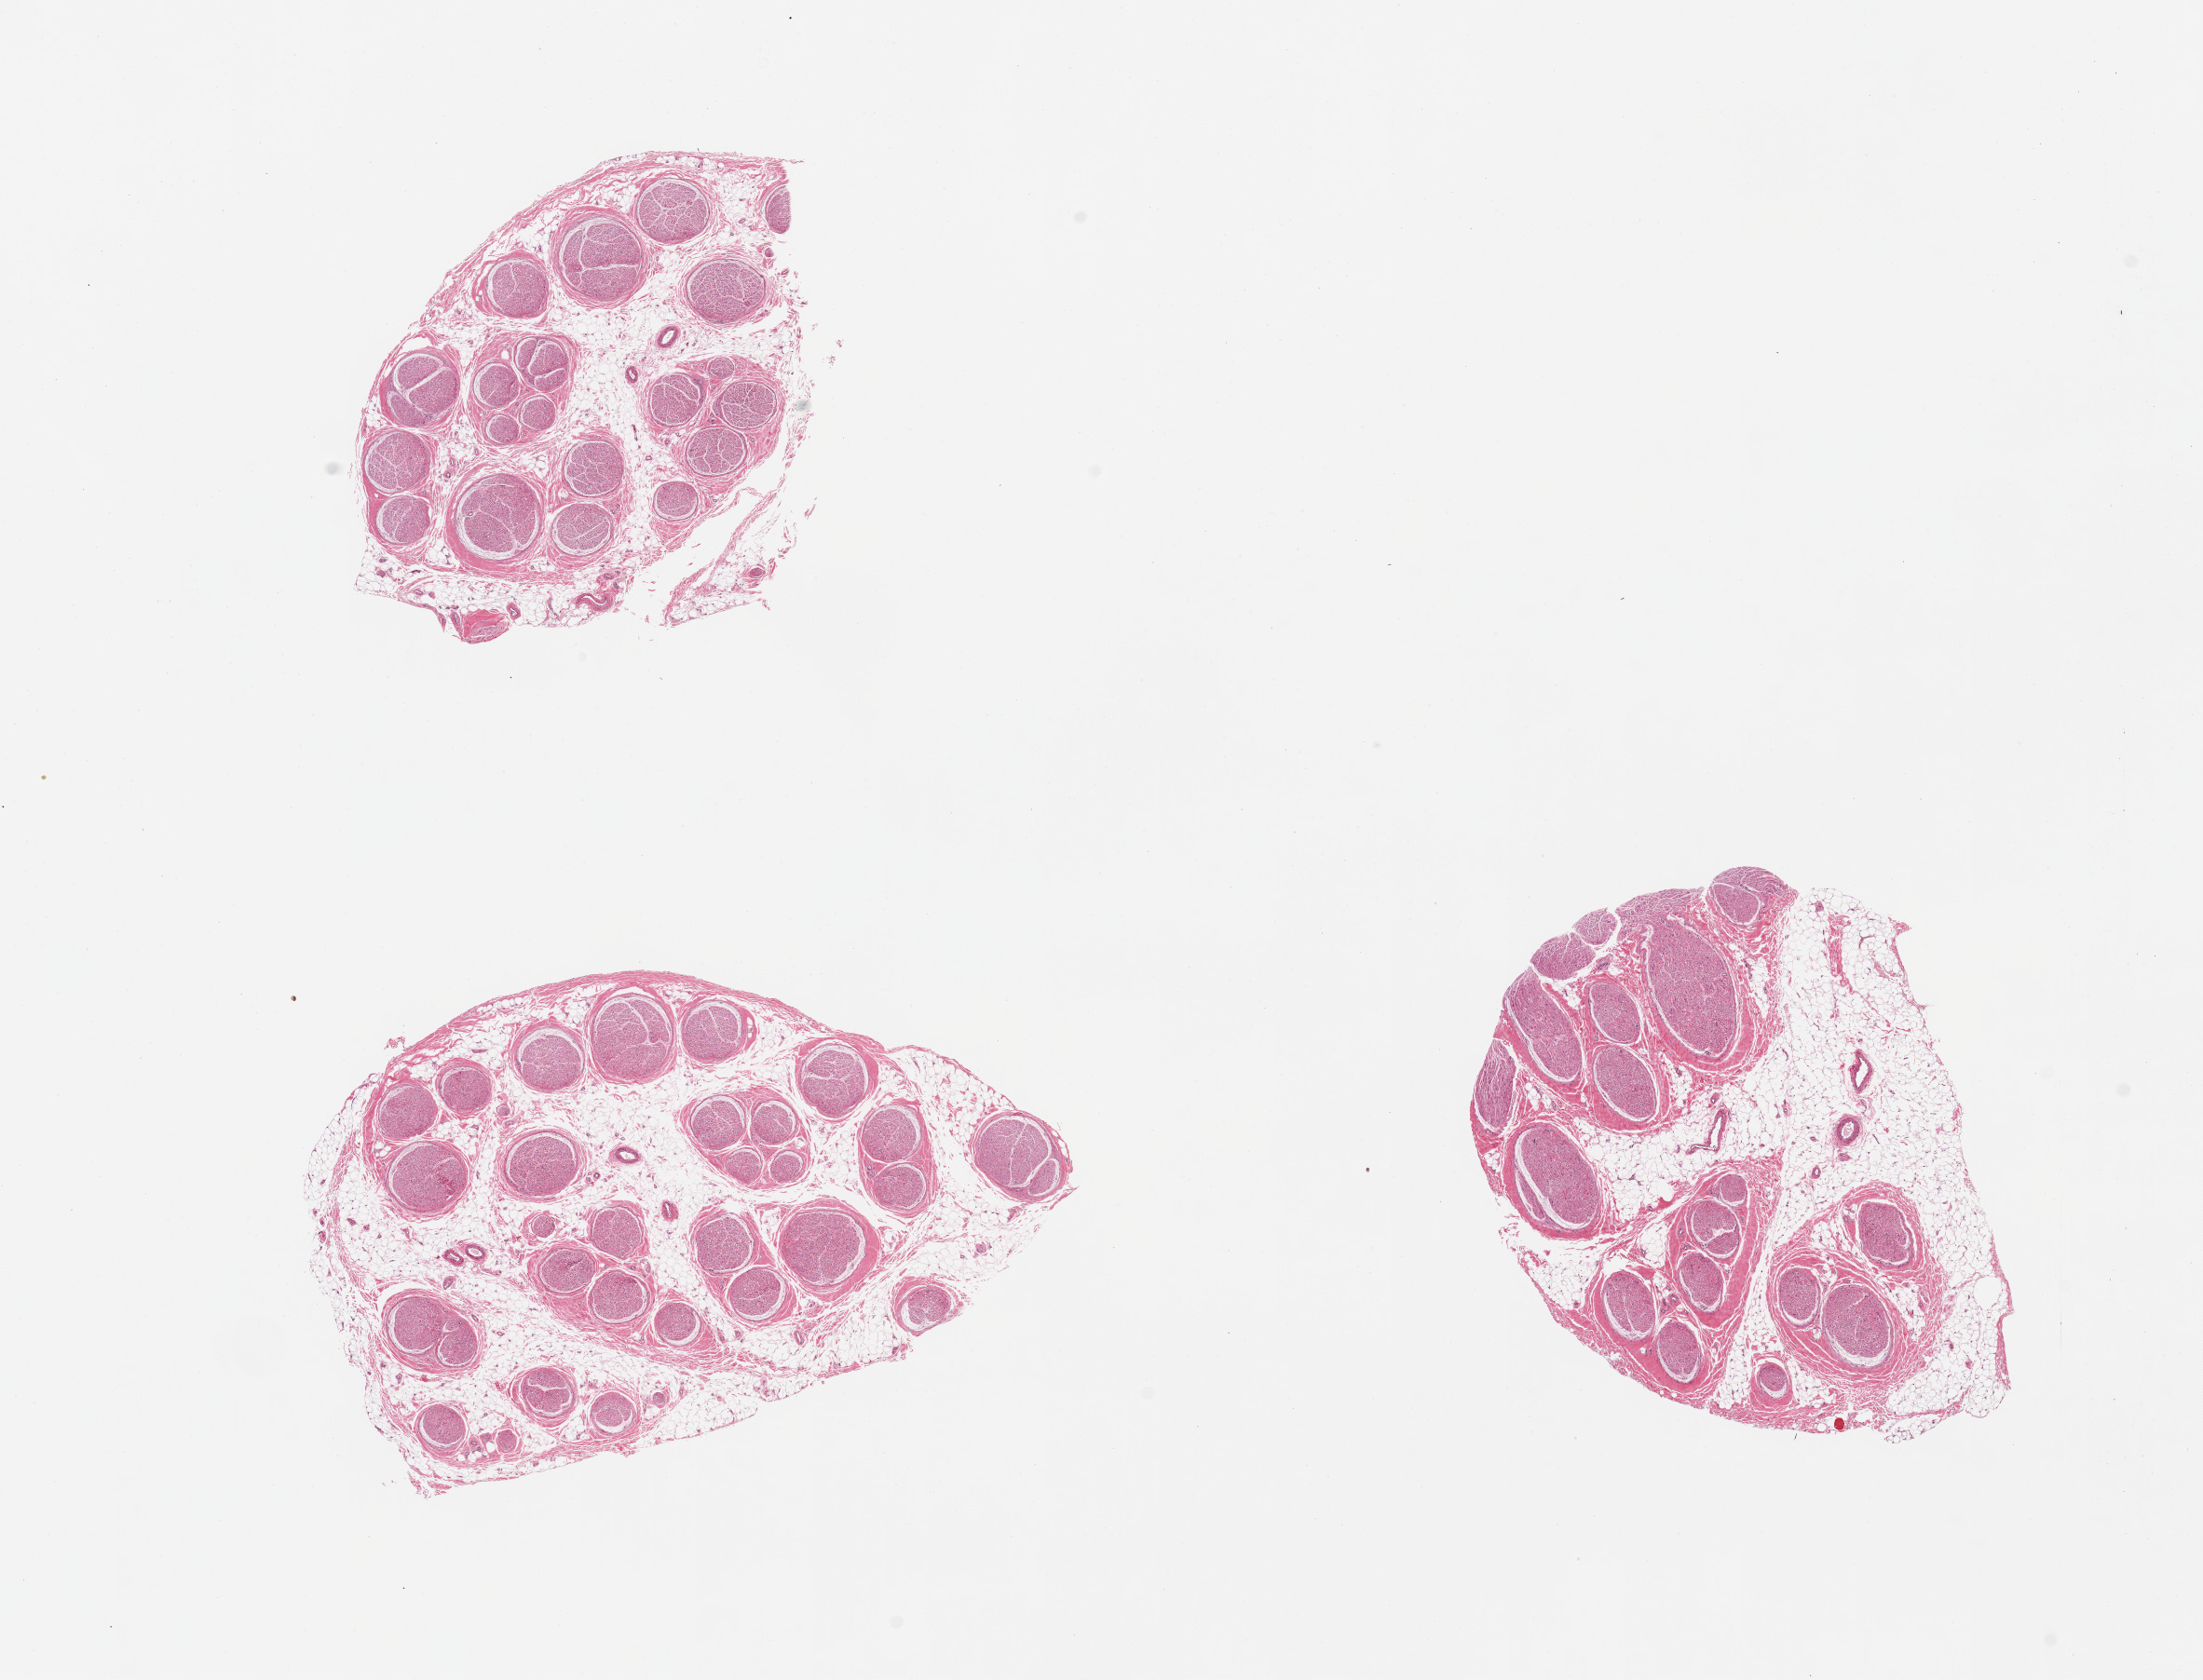
Hematoxylin and eosin (H&E) whole-slide image, brightfield, whole scanned area (about 18.7 x 14.3 mm) shown as a low-resolution overview, PAXgene-fixed paraffin-embedded (PFPE) section, section of tibial nerve (target tissue), donor tissue sample.
Reviewer comment on this tissue sample: 3 pieces; includes up to 40-50% internal and attached fat.